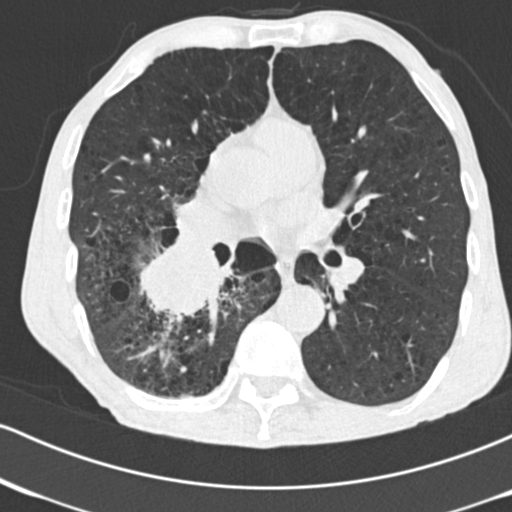
Low-dose screening chest CT, one axial slice; slice 87 of 182 in the series (ordered by position); 120 kVp; lung window (W 1500 / L -600 HU); 2 mm slice thickness; 512 × 512 image matrix, field of view 316 × 316 mm.
Annotated regions visible in this slice (expert manual segmentation):
- lesion 1 (tumor, lower lobe of right lung): bounding box (x1, y1, x2, y2) in pixels: (140, 240, 229, 317)